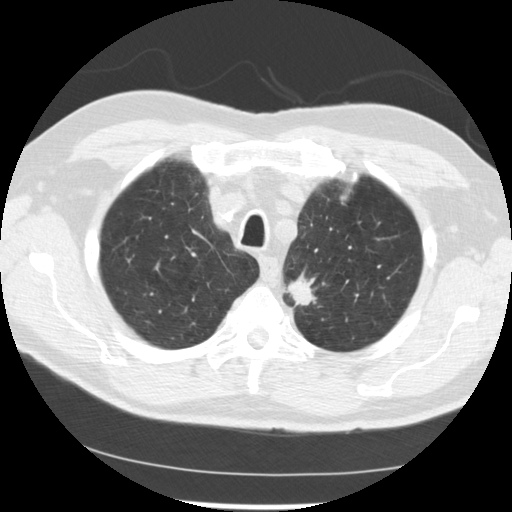
Low-dose screening chest CT, axial slice; baseline annual screen; lung window (W 1500 / L -600 HU); 2.5 mm slice thickness; 120 kVp; 512 × 512 image matrix, field of view 341 × 341 mm. Male participant, aged 71 years at enrolment. Current smoker at enrolment.
• Expert reader's lesion annotation, bounding box (x1, y1, x2, y2) in pixels: (273, 264, 335, 317).
• The screening reader recorded 2 non-calcified nodules or masses ≥4 mm on this exam (left upper lobe, left upper lobe); which of them this box marks is not recorded.
• Official screen result: positive, change unspecified: nodule(s) >= 4 mm or enlarging nodule(s), mass(es), or other non-specific abnormalities suspicious for lung cancer.
• Lung cancer was diagnosed 37 days after this screen: adenocarcinoma, NOS, left upper lobe, poorly differentiated (G3), stage IIIB (AJCC 6th edition), 25 mm at pathology.